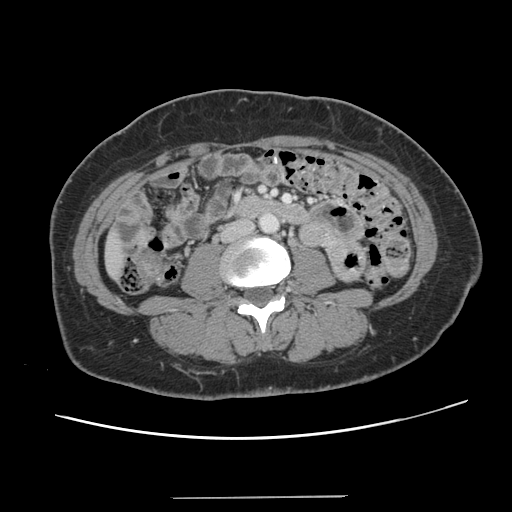
Contrast-enhanced abdominal CT, one axial slice; 120 kVp; intravenous contrast given; soft-tissue window (W 400 / L 40 HU); 2.5 mm slice thickness; 512 × 512 image matrix. Female patient, age 53 years. From the clinical record (not read from this slice): diagnosis: colorectal cancer liver metastases, imaged before liver resection; multiple liver metastases: no; largest metastasis: 14.5 cm; disease in both lobes: yes.
Outlined on this slice (expert manual segmentation):
- liver: bounding box (x1, y1, x2, y2) in pixels: (106, 234, 124, 277)
- planned liver remnant (the part of the liver to remain after resection): (107, 234, 124, 277)